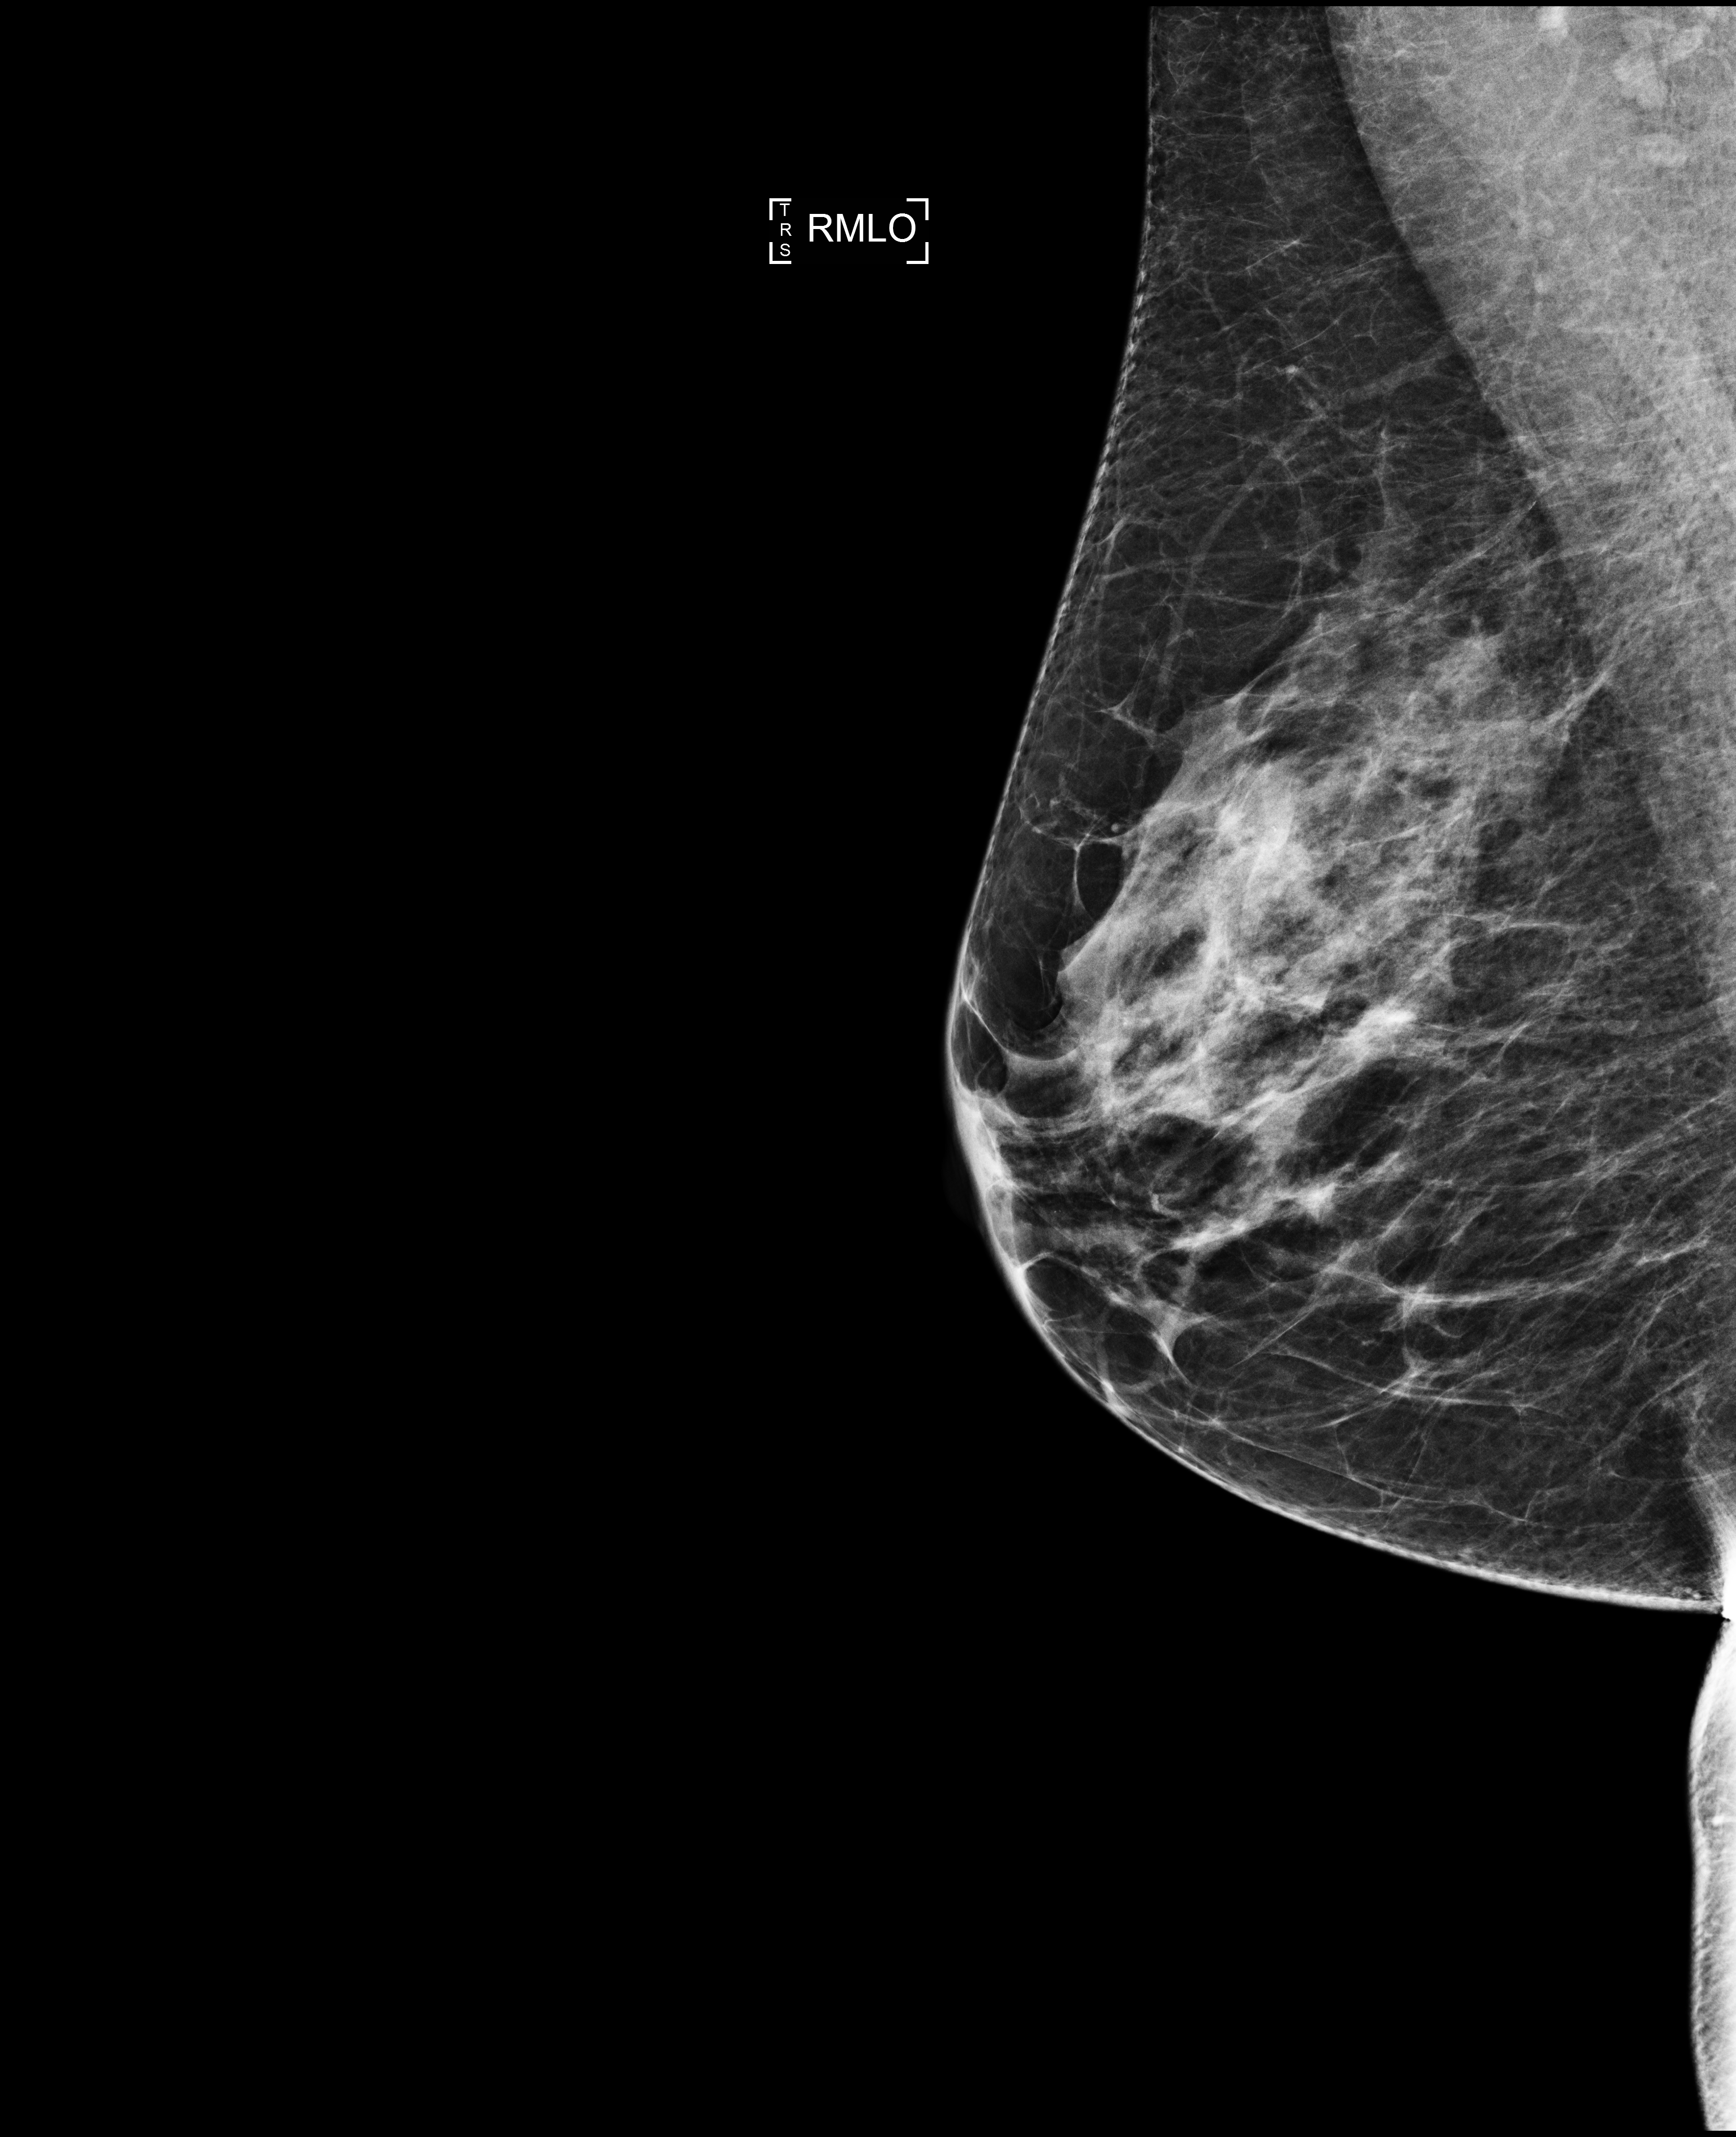
Screening examination; compressed breast thickness 57 mm; system: Selenia Dimensions. Patient aged 64 years (female).
Image type: full-field digital mammogram. Breast: right. Projection: mediolateral oblique (MLO) view.